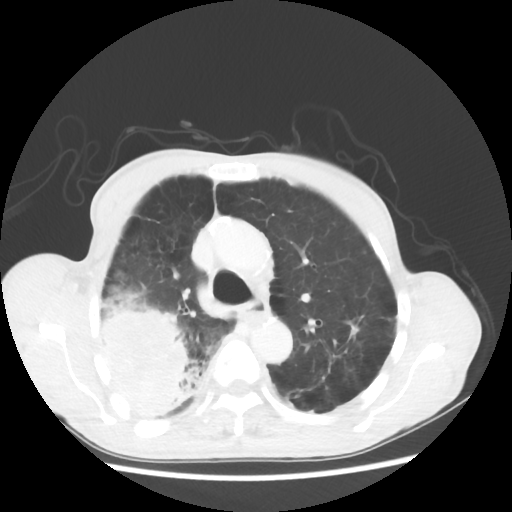
Chest CT, one axial slice; slice 38 of 58 in the series (ordered by position); reconstruction kernel STANDARD; 100 kVp; lung window (W 1500 / L -600 HU); 512 × 512 image matrix, field of view 351 × 351 mm. Male patient, age 75 years. Case-level facts recorded for this patient, not image findings: clinical TNM (as recorded): T4 N1 M1.
Structures marked on this image (bounding box drawn by a radiologist):
- lung tumour (recorded histology: adenocarcinoma): bounding box (x1, y1, x2, y2) in pixels: (96, 286, 206, 418)